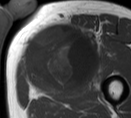
MRI of an extremity soft-tissue mass, one axial slice. MR volume resampled by the dataset authors to the PET/CT grid (not the native acquisition matrix). 131 × 118 image matrix, field of view 128 × 115 mm. Male patient. Case-level facts recorded for this patient, not image findings: histological type: pleiomorphic liposarcoma; grade: high; site of the primary tumour: left thigh.
Structures marked on this image (expert contour drawn on MRI and transferred to this co-registered scan by the dataset authors):
- gross tumour volume including surrounding oedema: bounding box [x1, y1, x2, y2] px = [25, 18, 99, 85]
- gross tumour volume (mass): [25, 27, 94, 85]